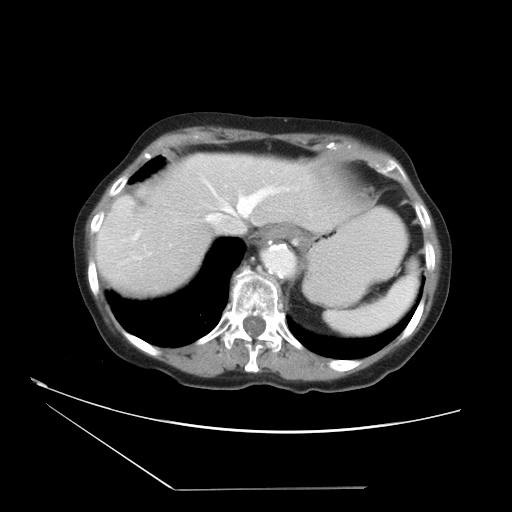
Contrast-enhanced abdominal CT, one axial slice; position 29 of 36 along the scan axis; 120 kVp; intravenous contrast given; soft-tissue window (W 400 / L 40 HU); 5 mm slice thickness; 512 × 512 image matrix. Female patient, age 81 years. Case-level facts recorded for this patient, not image findings: diagnosis: colorectal cancer liver metastases, imaged before liver resection; multiple liver metastases: no; largest metastasis: 1.6 cm; disease in both lobes: no.
Structures marked on this image (manually delineated by an expert):
- hepatic veins: bounding box (x1, y1, x2, y2) in pixels: (206, 186, 289, 223)
- liver: (96, 153, 369, 298)
- planned liver remnant (the part of the liver to remain after resection): (96, 153, 369, 299)